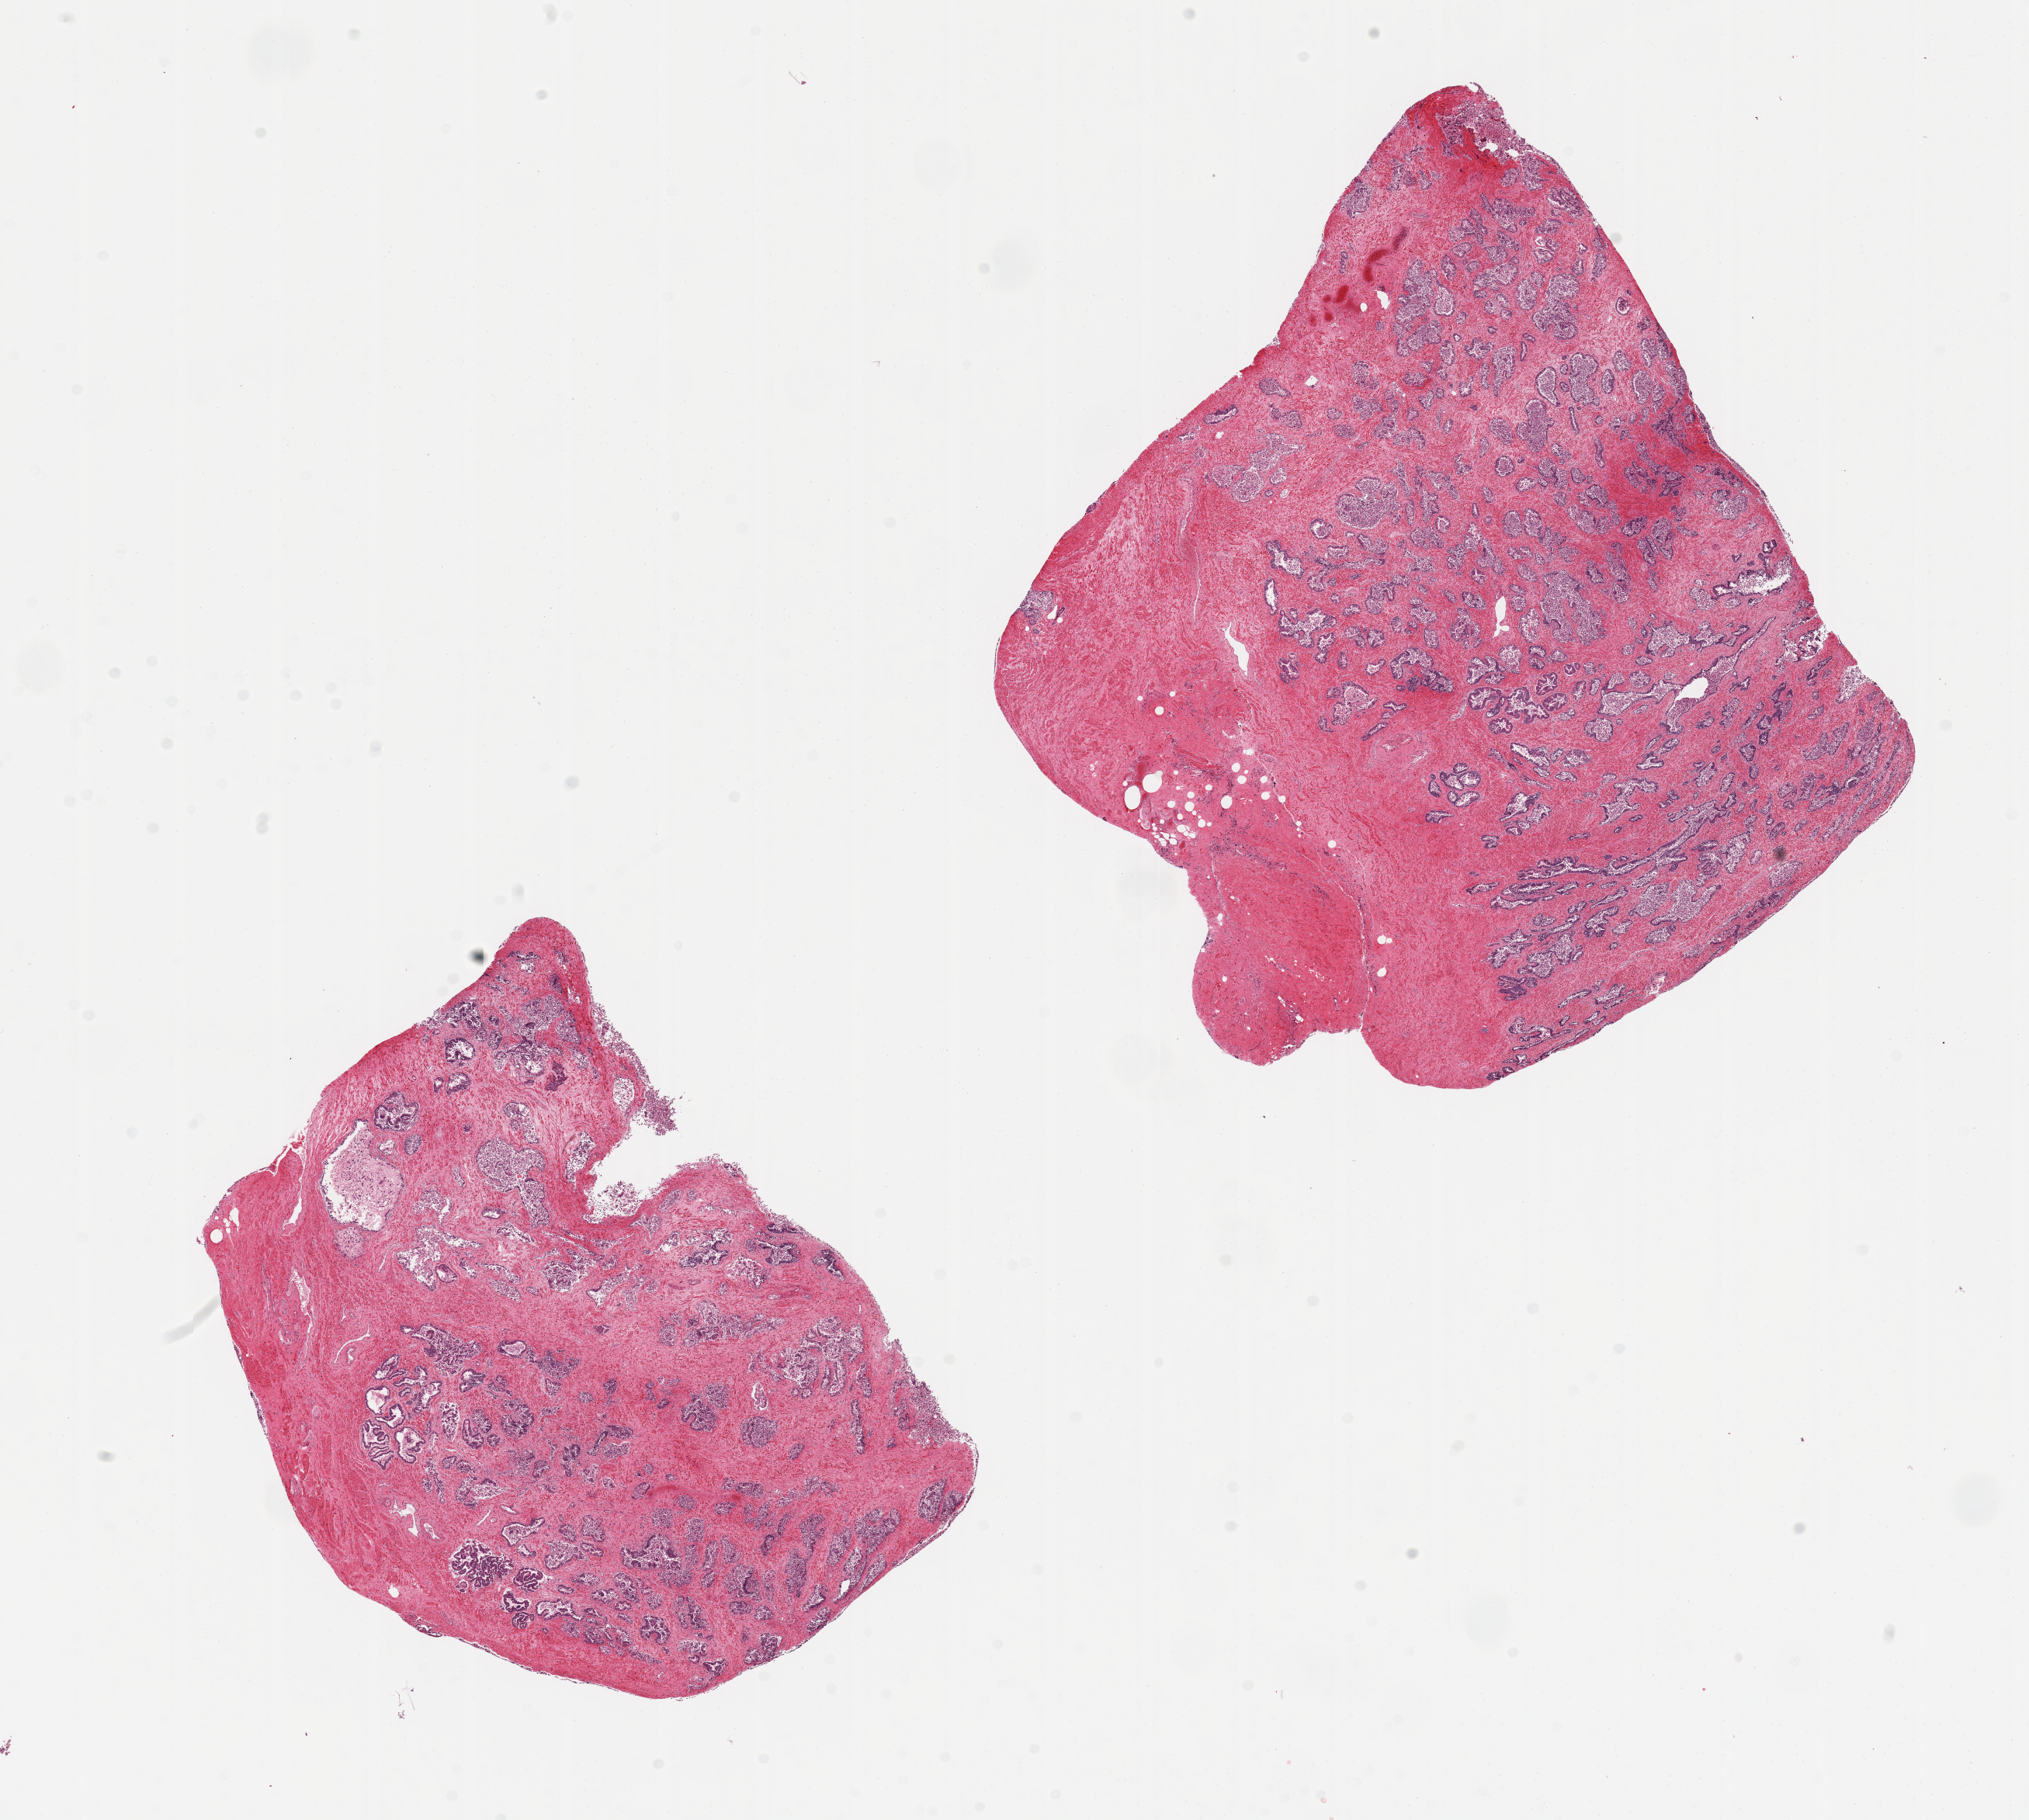
Digitized haematoxylin and eosin-stained section — low-resolution overview of the scanned area, about 20.7 x 18.5 mm (slide scanned at 20x), PAXgene-fixed paraffin-embedded (PFPE) section, sampled site (target tissue): prostate, donor tissue sample.
Reviewer comment on this tissue sample: 2 pieces; glands autolyzed.